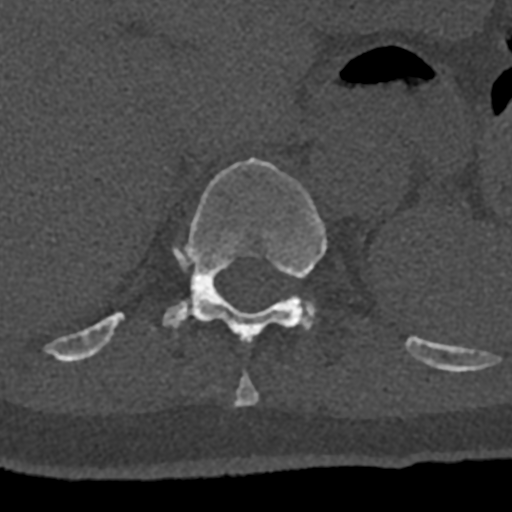
CT including the spine, one axial slice. Position 547 of 797 along the scan axis. Bone window (W 1800 / L 400 HU). 0.5 mm slice thickness. 512 × 512 image matrix, field of view 160 × 160 mm. Male patient, age 74 years. Case-level facts recorded for this patient, not image findings: primary cancer: renal.
Structures marked on this image (semi-automatically segmented with operator editing):
- T10 vertebra: bounding box (x1, y1, x2, y2) in pixels: (233, 372, 259, 407)
- T11 vertebra: (70, 157, 432, 367)
- T12 vertebra: (303, 301, 316, 324)